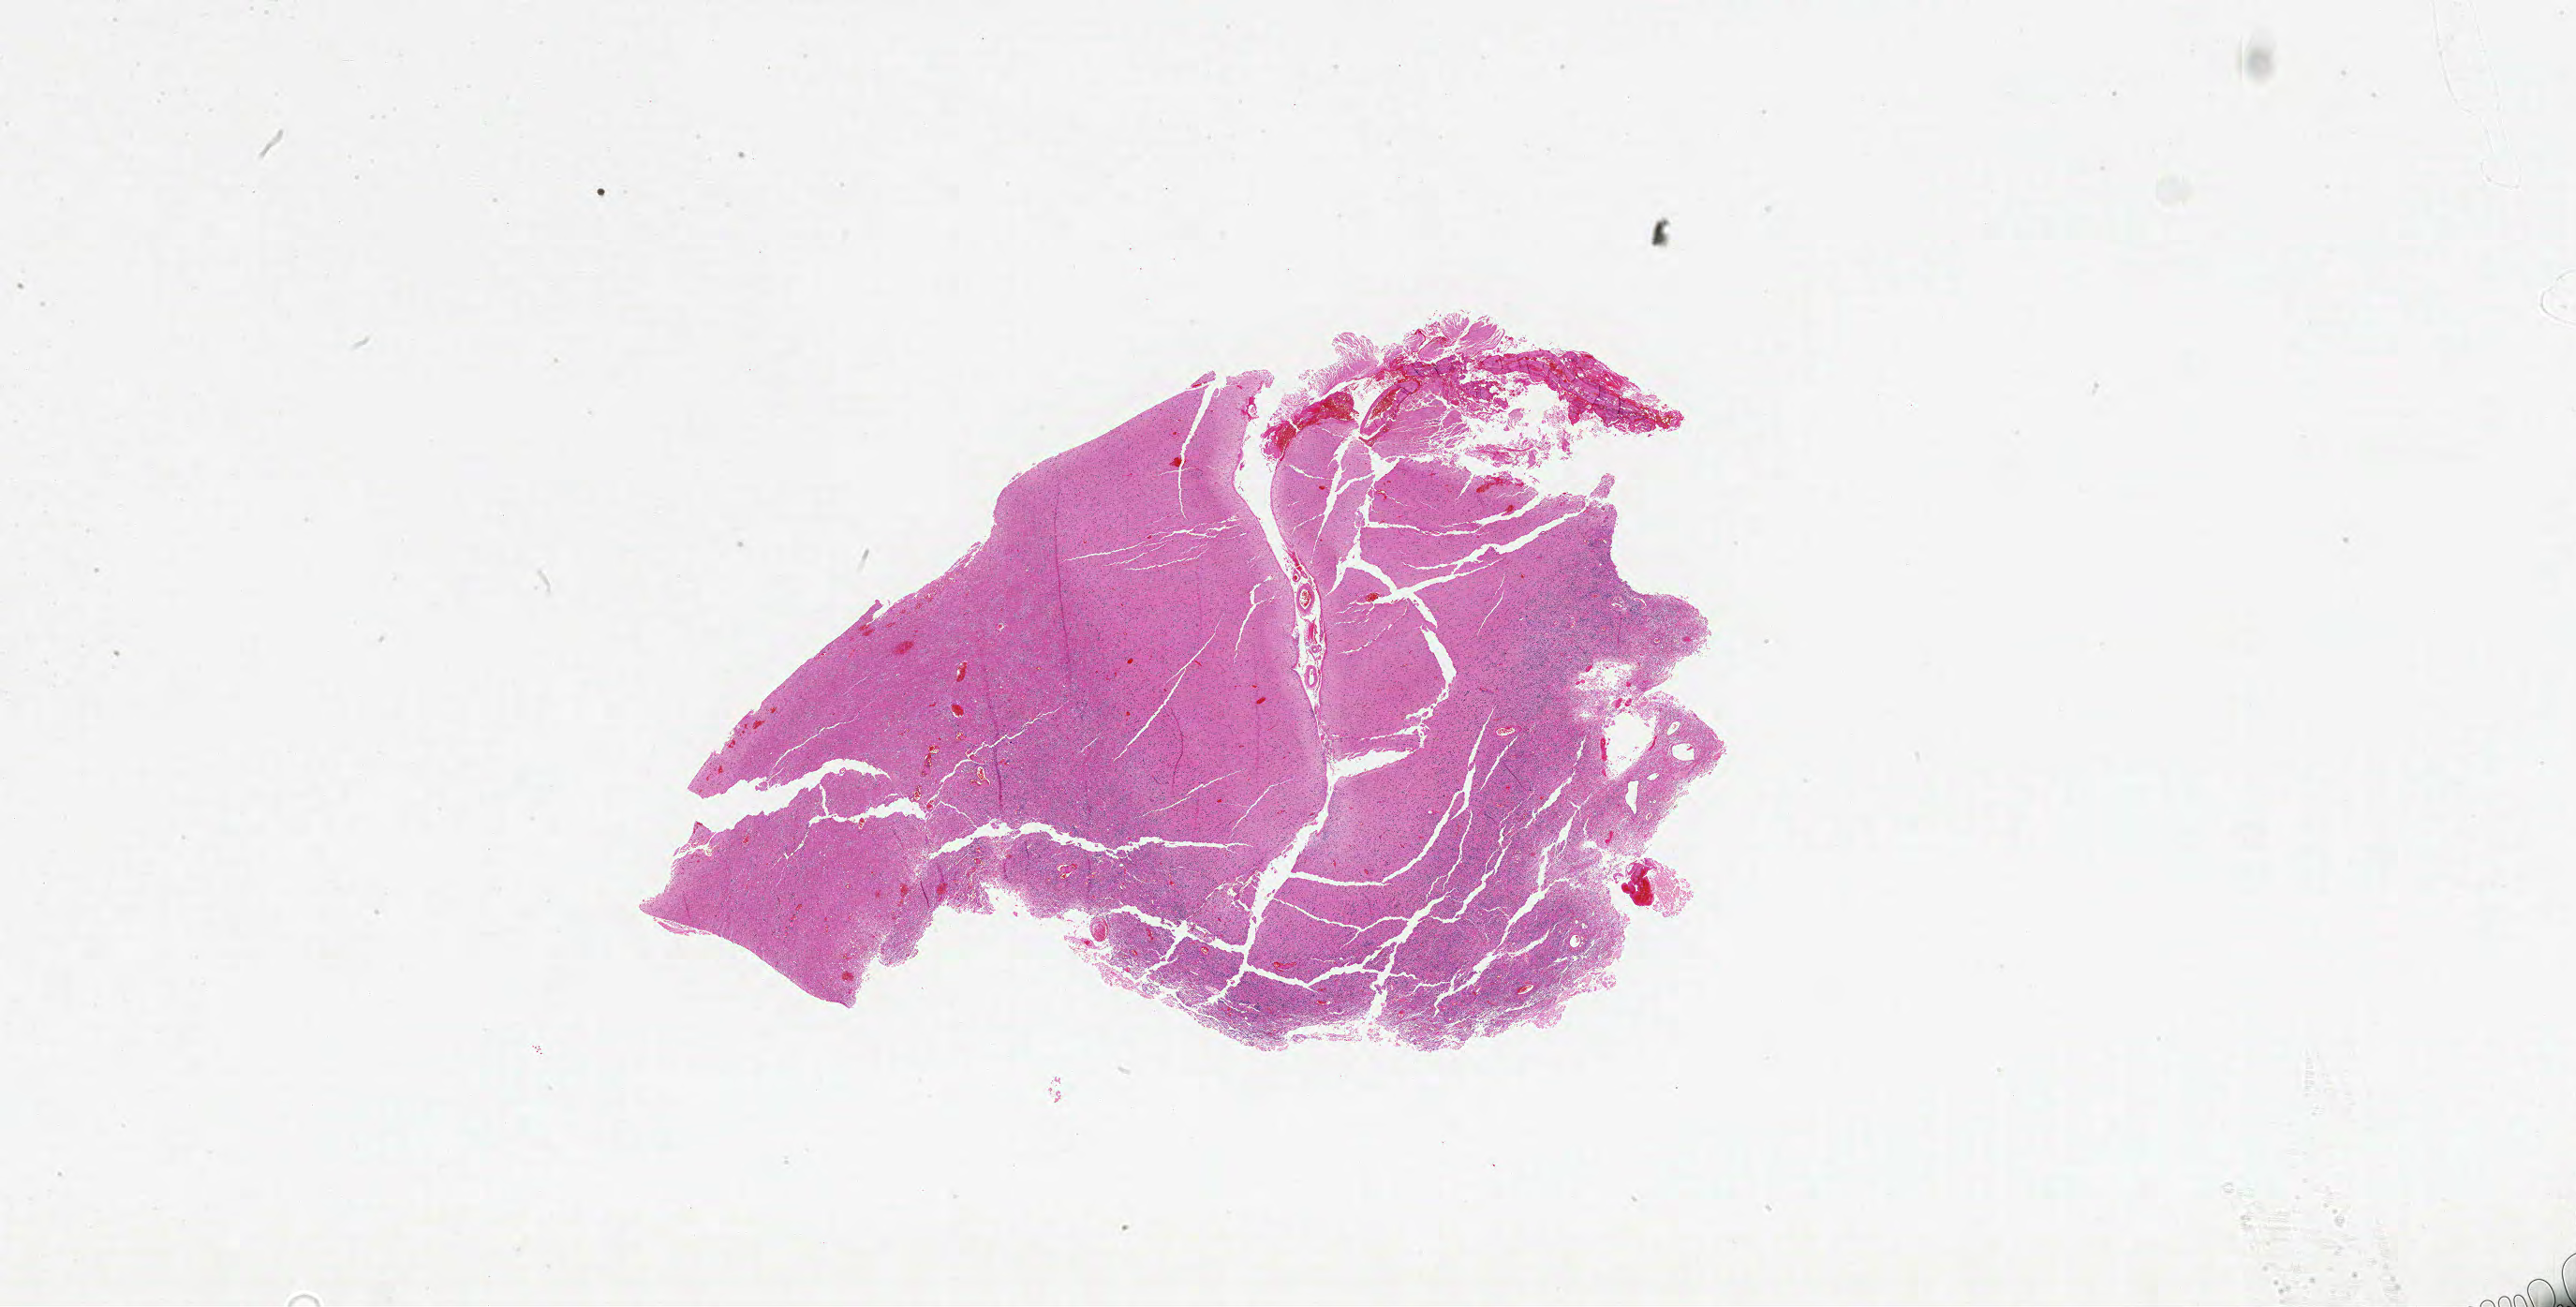
H&E whole-slide image, a low-resolution overview of the entire scanned area, about 44.0 x 22.3 mm (from a 20x scan). Formalin-fixed paraffin-embedded (FFPE) diagnostic section. Brain, primary tumour sample. Female patient; age at initial diagnosis 68 years.
Histologic diagnosis: Glioblastoma.